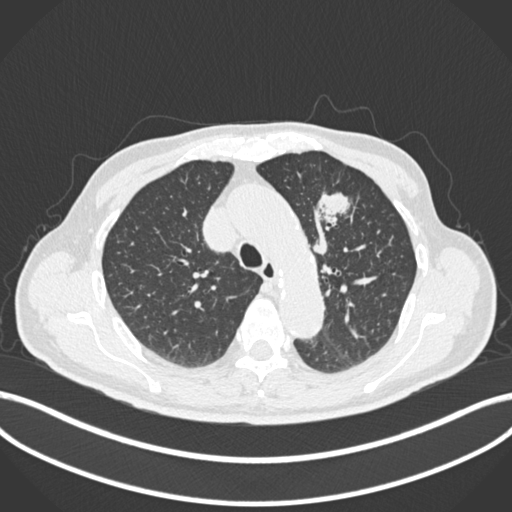
Chest CT, one axial slice. Slice 181 of 261 in the series (ordered by position). Reconstruction kernel B30f. 120 kVp. Lung window (W 1500 / L -600 HU). 1 mm slice thickness. 512 × 512 image matrix. Male patient, age 74 years. Case-level facts recorded for this patient, not image findings: clinical TNM (as recorded): T2b N0 M1c.
Structures marked on this image (bounding box drawn by a radiologist):
- lung tumour (recorded histology: adenocarcinoma): box from (x=313, y=189) to (x=354, y=226) px